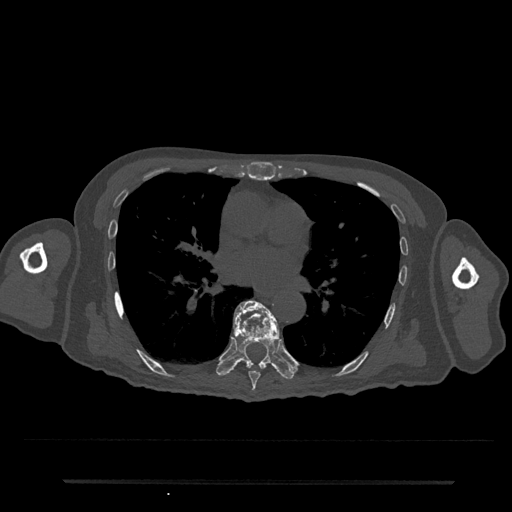
CT including the spine, one axial slice; position 447 of 797 along the scan axis; reconstruction kernel Br40s/3; bone window (W 1800 / L 400 HU); 512 × 512 image matrix, field of view 427 × 427 mm. Male patient, age 74 years. Case-level facts recorded for this patient, not image findings: primary cancer: prostate.
Annotated regions visible in this slice (semi-automatic segmentation, software-assisted and operator-edited):
- T7 vertebra: bounding box (x1, y1, x2, y2) in pixels: (234, 302, 273, 391)
- T8 vertebra: (216, 300, 295, 380)